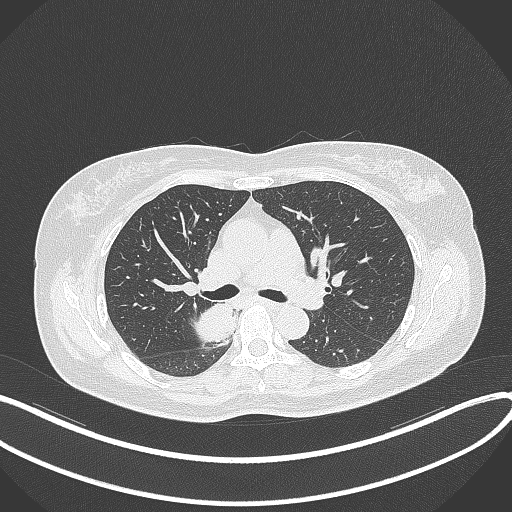
Chest CT, one axial slice; 120 kVp; lung window (W 1500 / L -600 HU); 1 mm slice thickness; 512 × 512 image matrix. Patient: female, 54 years. Case-level facts recorded for this patient, not image findings: clinical TNM (as recorded): T4 N0 M0.
Structures marked on this image (rectangle marked by the reading radiologist):
- lung tumour (recorded histology: adenocarcinoma): bounding box <190,300,240,347> (left, top, right, bottom; pixels)